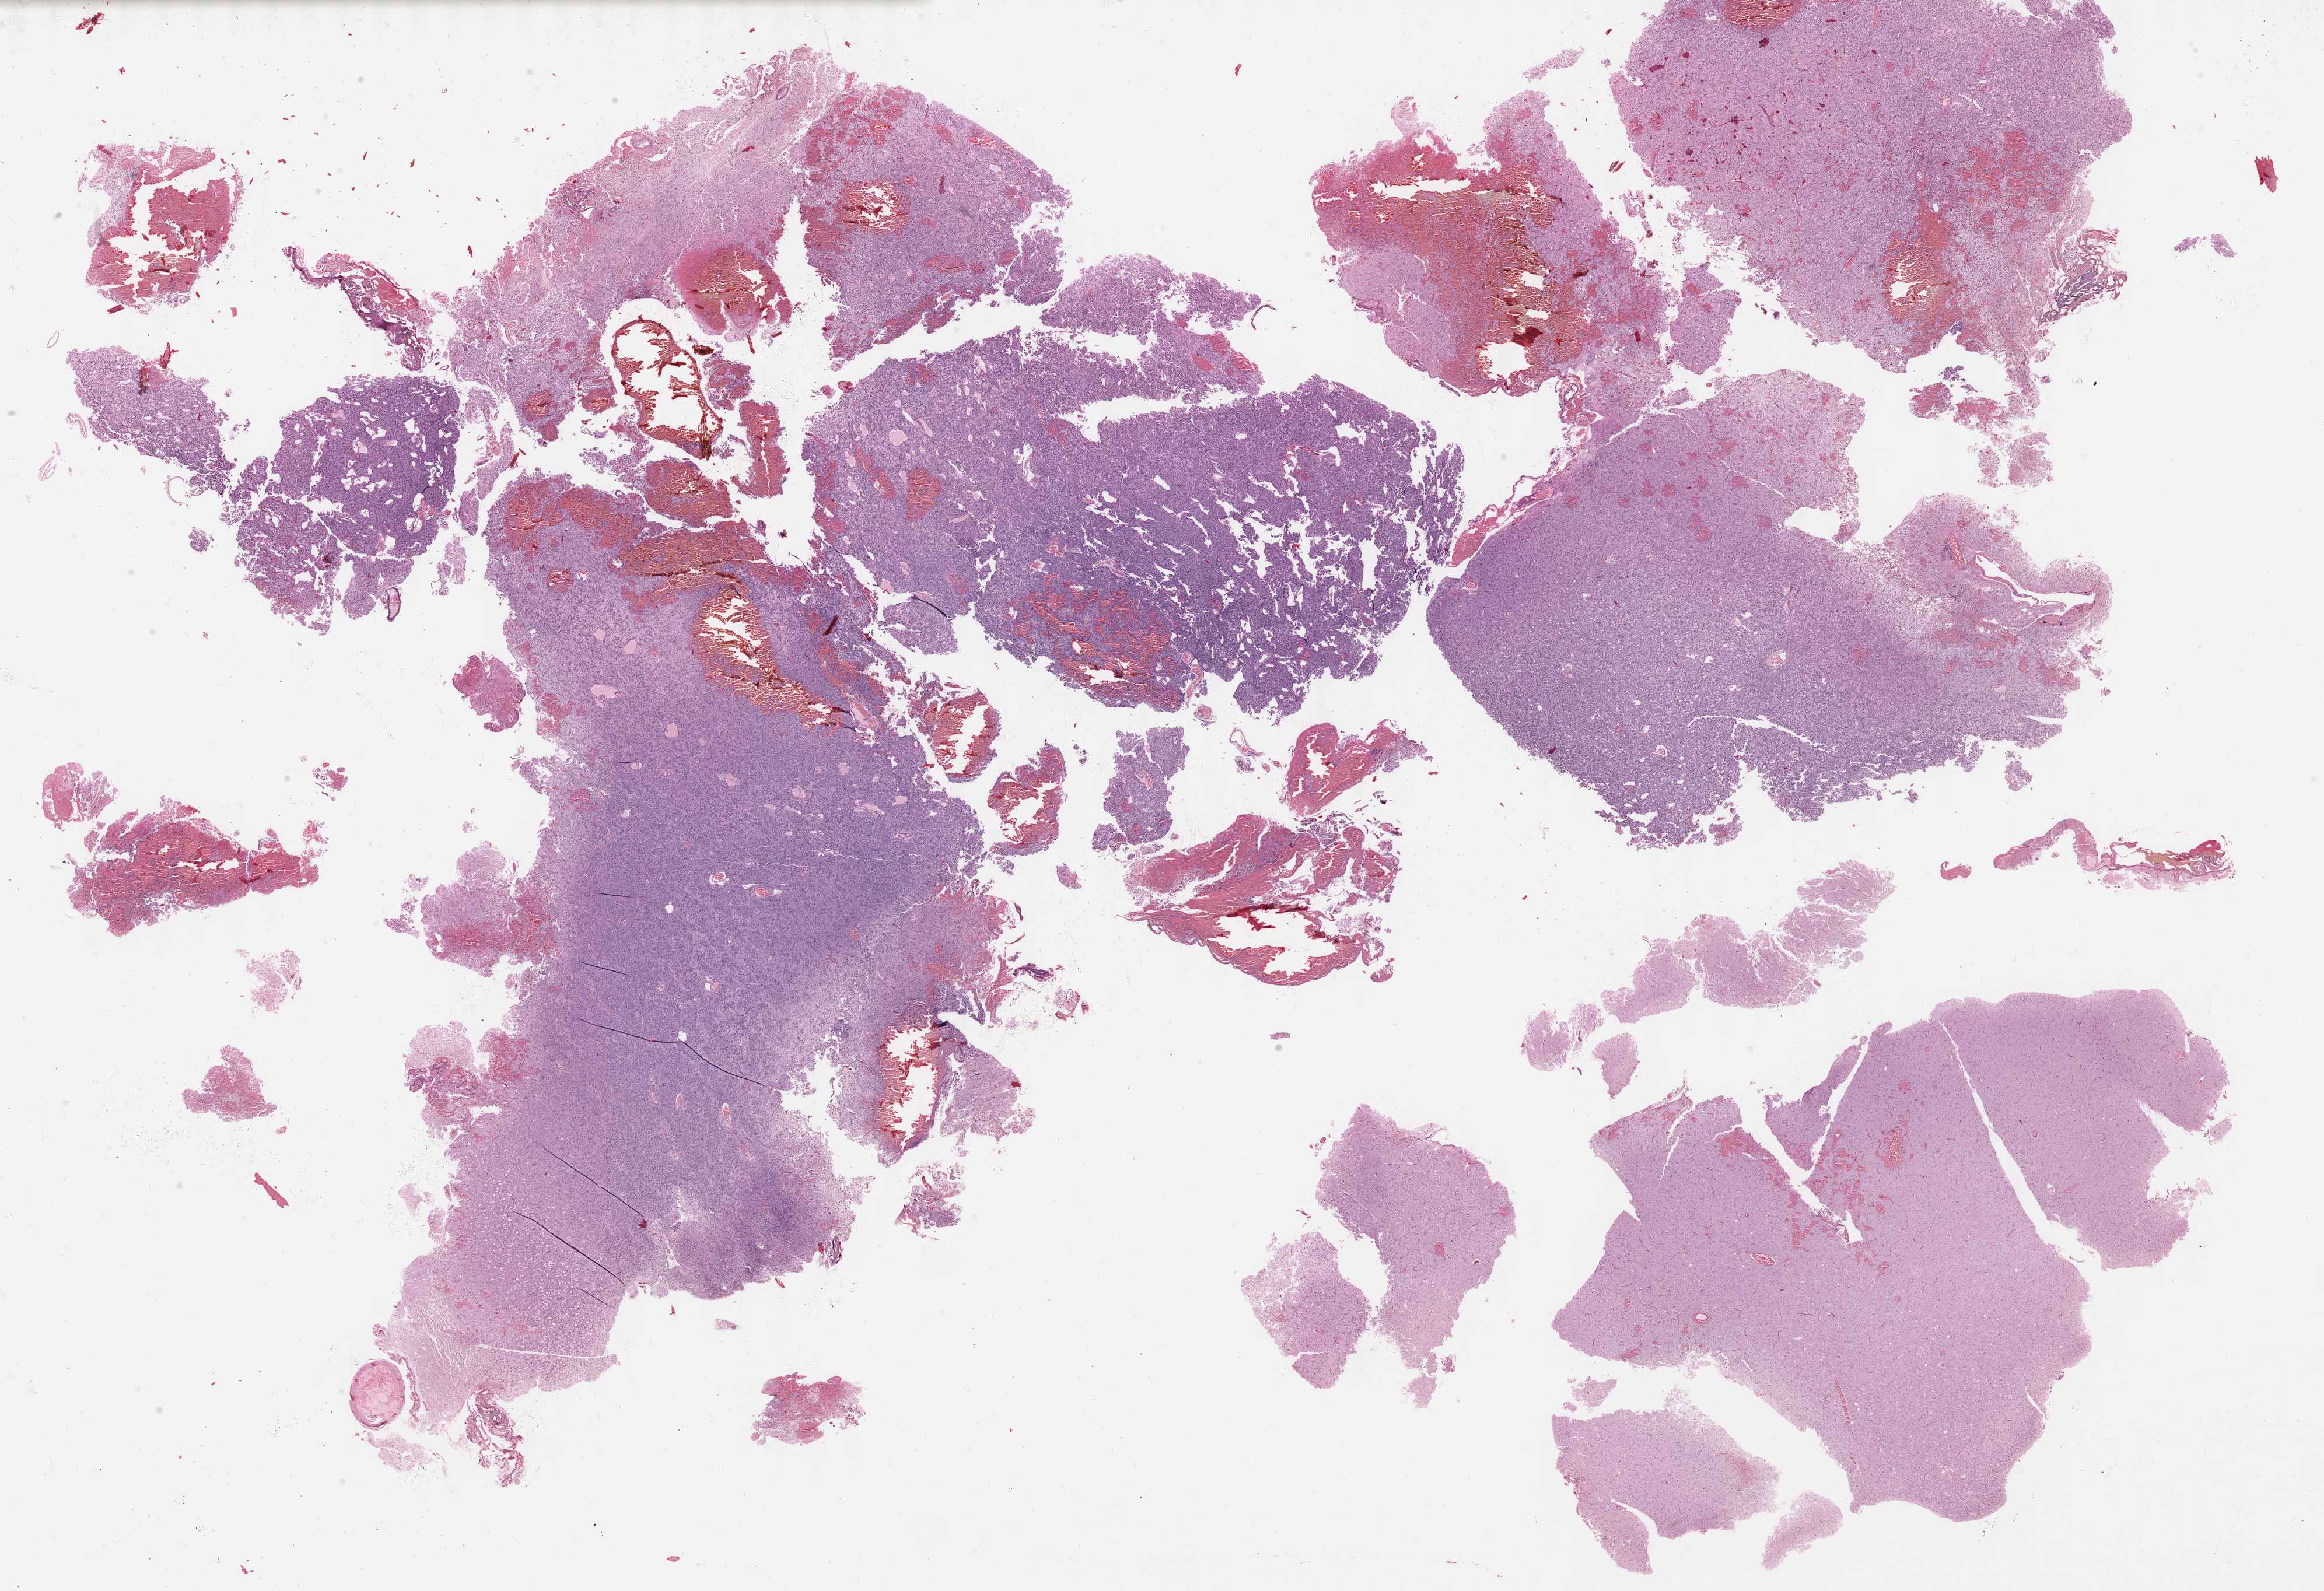
Whole-slide histology image, H&E-stained, low-resolution overview of the scanned area, about 32.2 x 22.0 mm (slide scanned at 40x), FFPE section, sample: primary tumour, brain. Patient: male, age at initial diagnosis 29 years. Histologic grade: G2 (moderately differentiated).
- diagnosis: Mixed glioma (cerebrum)